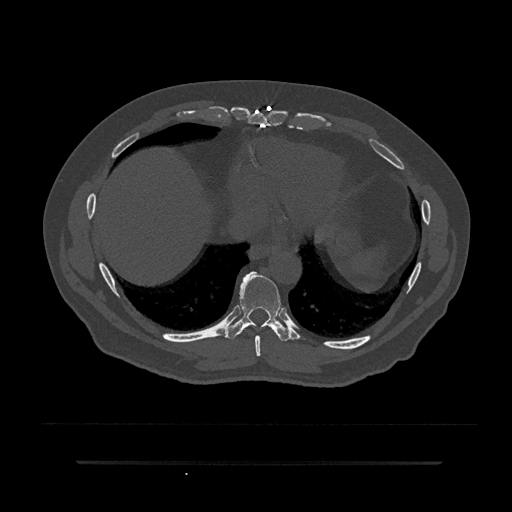
CT including the spine, one axial slice; position 392 of 797 along the scan axis; reconstruction kernel Br40s/3; bone window (W 1800 / L 400 HU); 0.5 mm slice thickness; 512 × 512 image matrix, field of view 464 × 464 mm. Male patient, age 59 years. Case-level facts recorded for this patient, not image findings: primary cancer: bile ducts; vertebrae with lytic lesions (as recorded): T10.
Annotated regions visible in this slice (semi-automatically segmented with operator editing):
- T8 vertebra: bounding box <255,335,261,356> (left, top, right, bottom; pixels)
- T9 vertebra: <227,271,291,341>